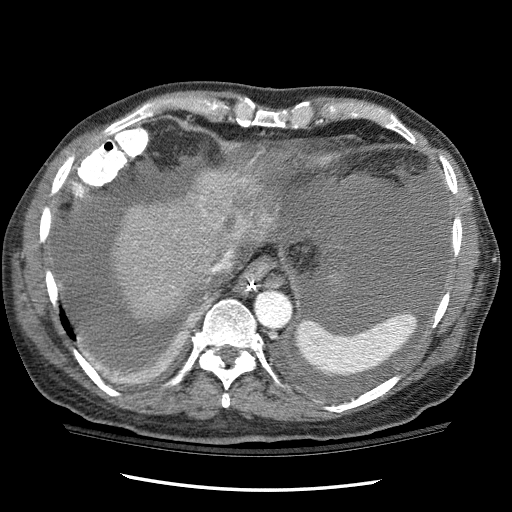
Contrast-enhanced abdominal CT (liver protocol), one axial slice; slice 93 of 114 in the series (ordered by position); reconstruction kernel STANDARD; 120 kVp; one of 3 acquisitions stored at this slice position; soft-tissue window (W 400 / L 40 HU); 2.5 mm slice thickness; 512 × 512 image matrix. From the clinical record (not read from this slice): diagnosis: hepatocellular carcinoma (patient treated with transarterial chemoembolisation; whether this scan precedes or follows treatment is not stated here); TNM stage (as recorded): Stage-I; Child-Pugh class: C; tumour differentiation: well differentiated.
Annotated regions visible in this slice (semi-automatic segmentation, software-assisted and operator-edited):
- liver parenchyma outside the tumour (the mass and vessels are separate outlines, so this box may not span the whole liver): bounding box [x1, y1, x2, y2] px = [114, 167, 281, 321]
- mass: [196, 172, 282, 236]
- liver vessels: [226, 252, 230, 256]